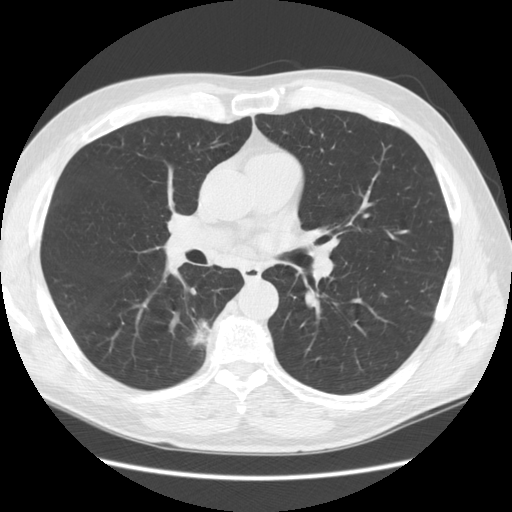
Low-dose screening chest CT, one axial slice; position 73 of 133 along the scan axis; 120 kVp; lung window (W 1500 / L -600 HU); 2.5 mm slice thickness; 512 × 512 image matrix, field of view 370 × 370 mm.
Structures marked on this image (outlined manually by an expert reader):
- lesion 1 (tumor, lower lobe of right lung): bounding box [x1, y1, x2, y2] px = [191, 319, 213, 347]